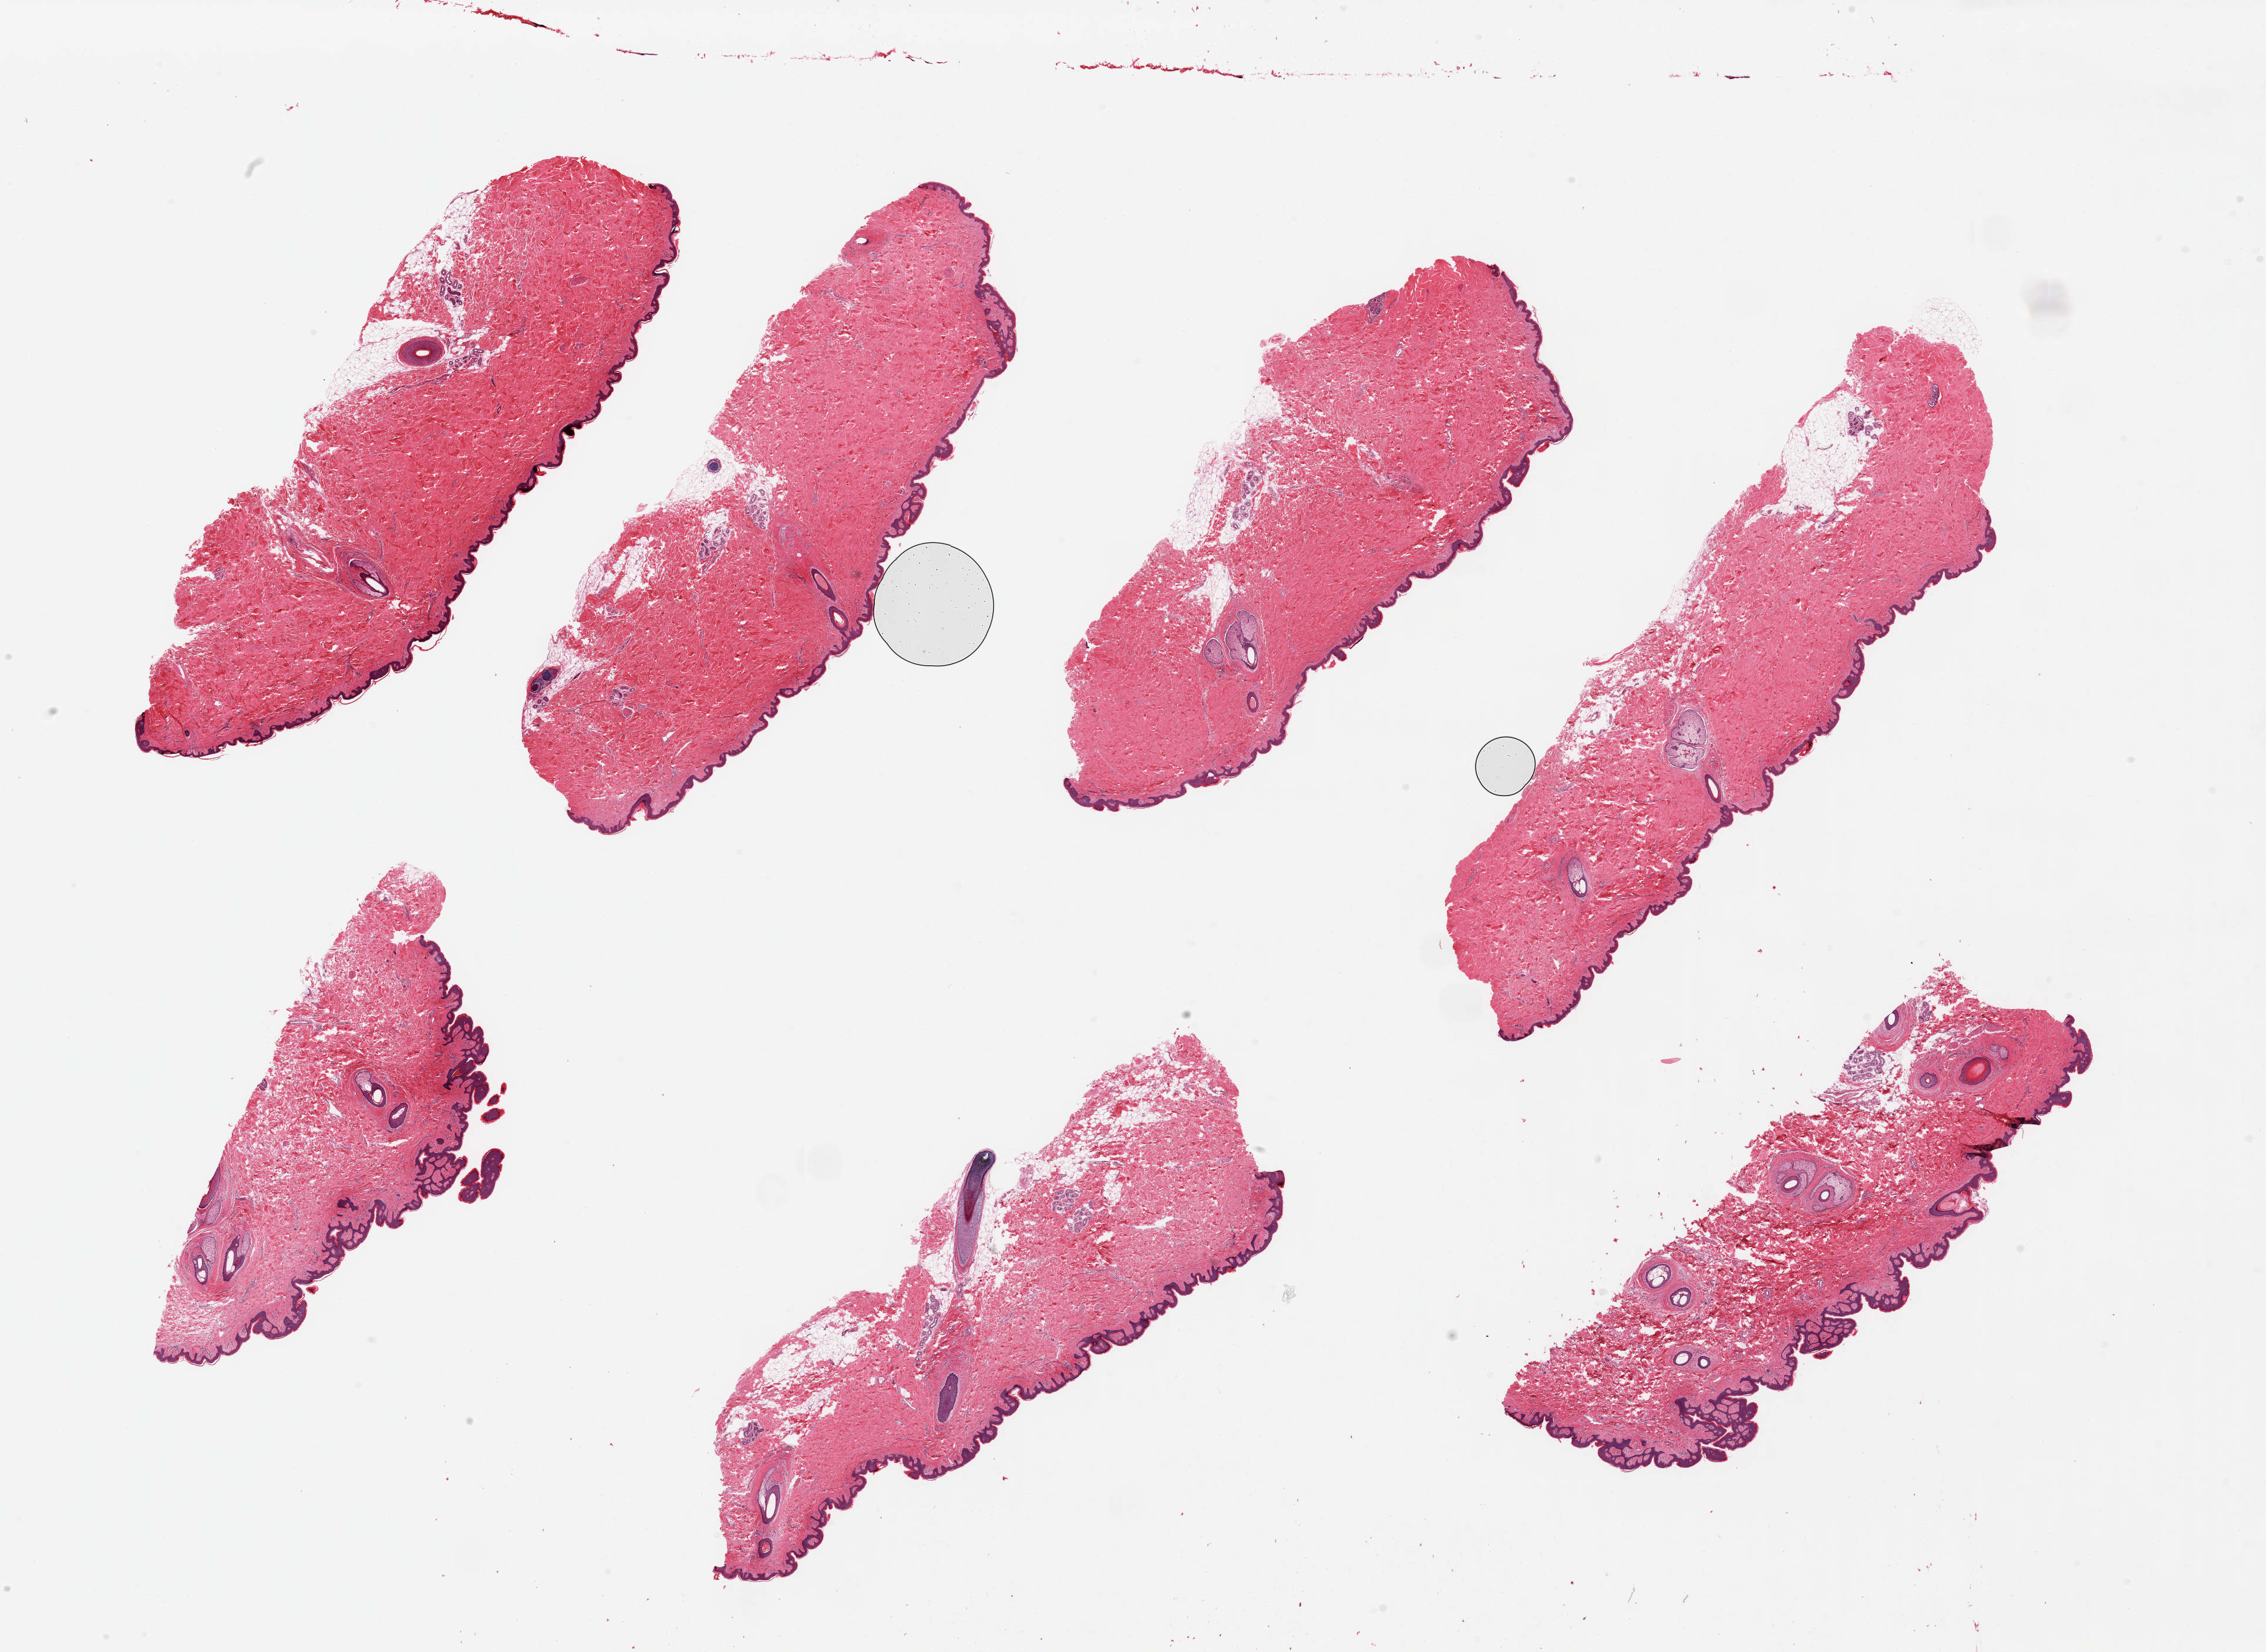
Whole-slide image, haematoxylin and eosin stain, whole scanned area (about 30.5 x 22.3 mm, slide scanned at 20x) shown as a low-resolution overview; PAXgene-fixed paraffin-embedded (PFPE) section; section of skin of suprapubic region (target tissue); donor tissue sample. Donor sex: male.
* review note (as recorded): 7 pieces, trace dermal fat; squamous epithelium is ~40 microns